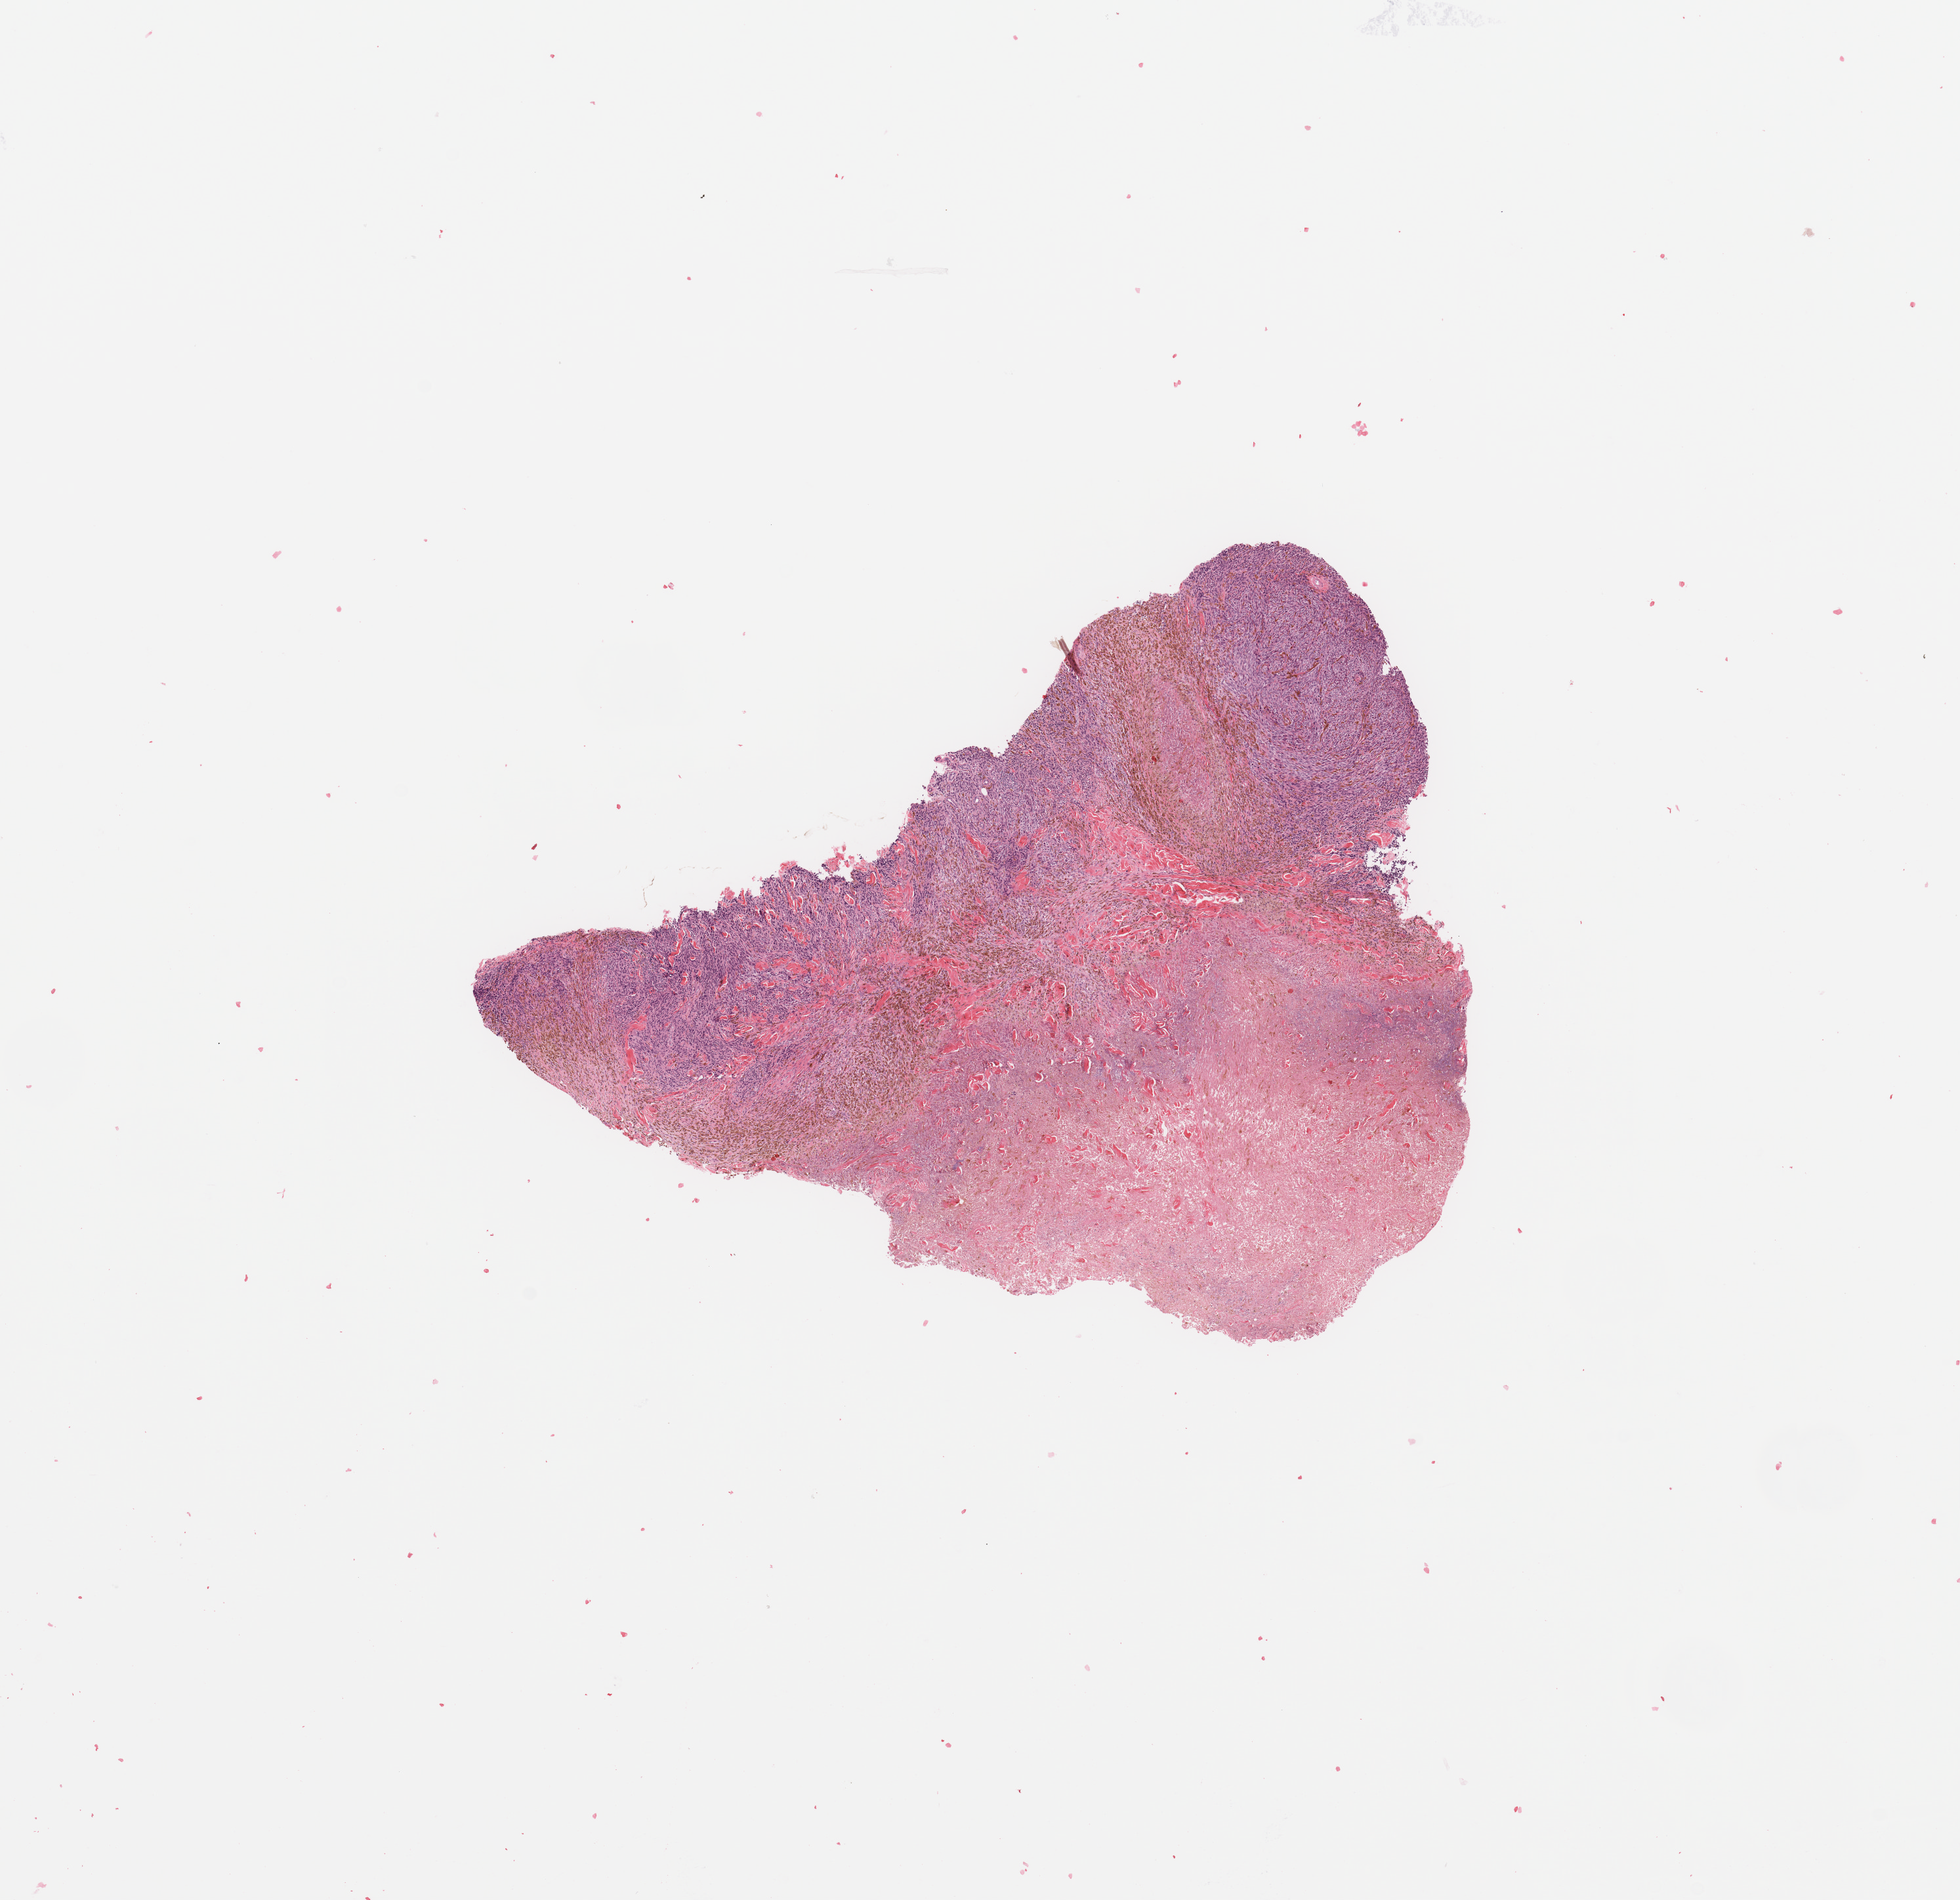
H&E whole-slide image — low-resolution overview of the scanned area, about 11.8 x 11.4 mm, melanoma tumour tissue; sampled site not recorded. 45-year-old female patient.
* primary tumour site (as recorded): trunk
* patient diagnosis (cohort enrolment): cutaneous melanoma (skin)